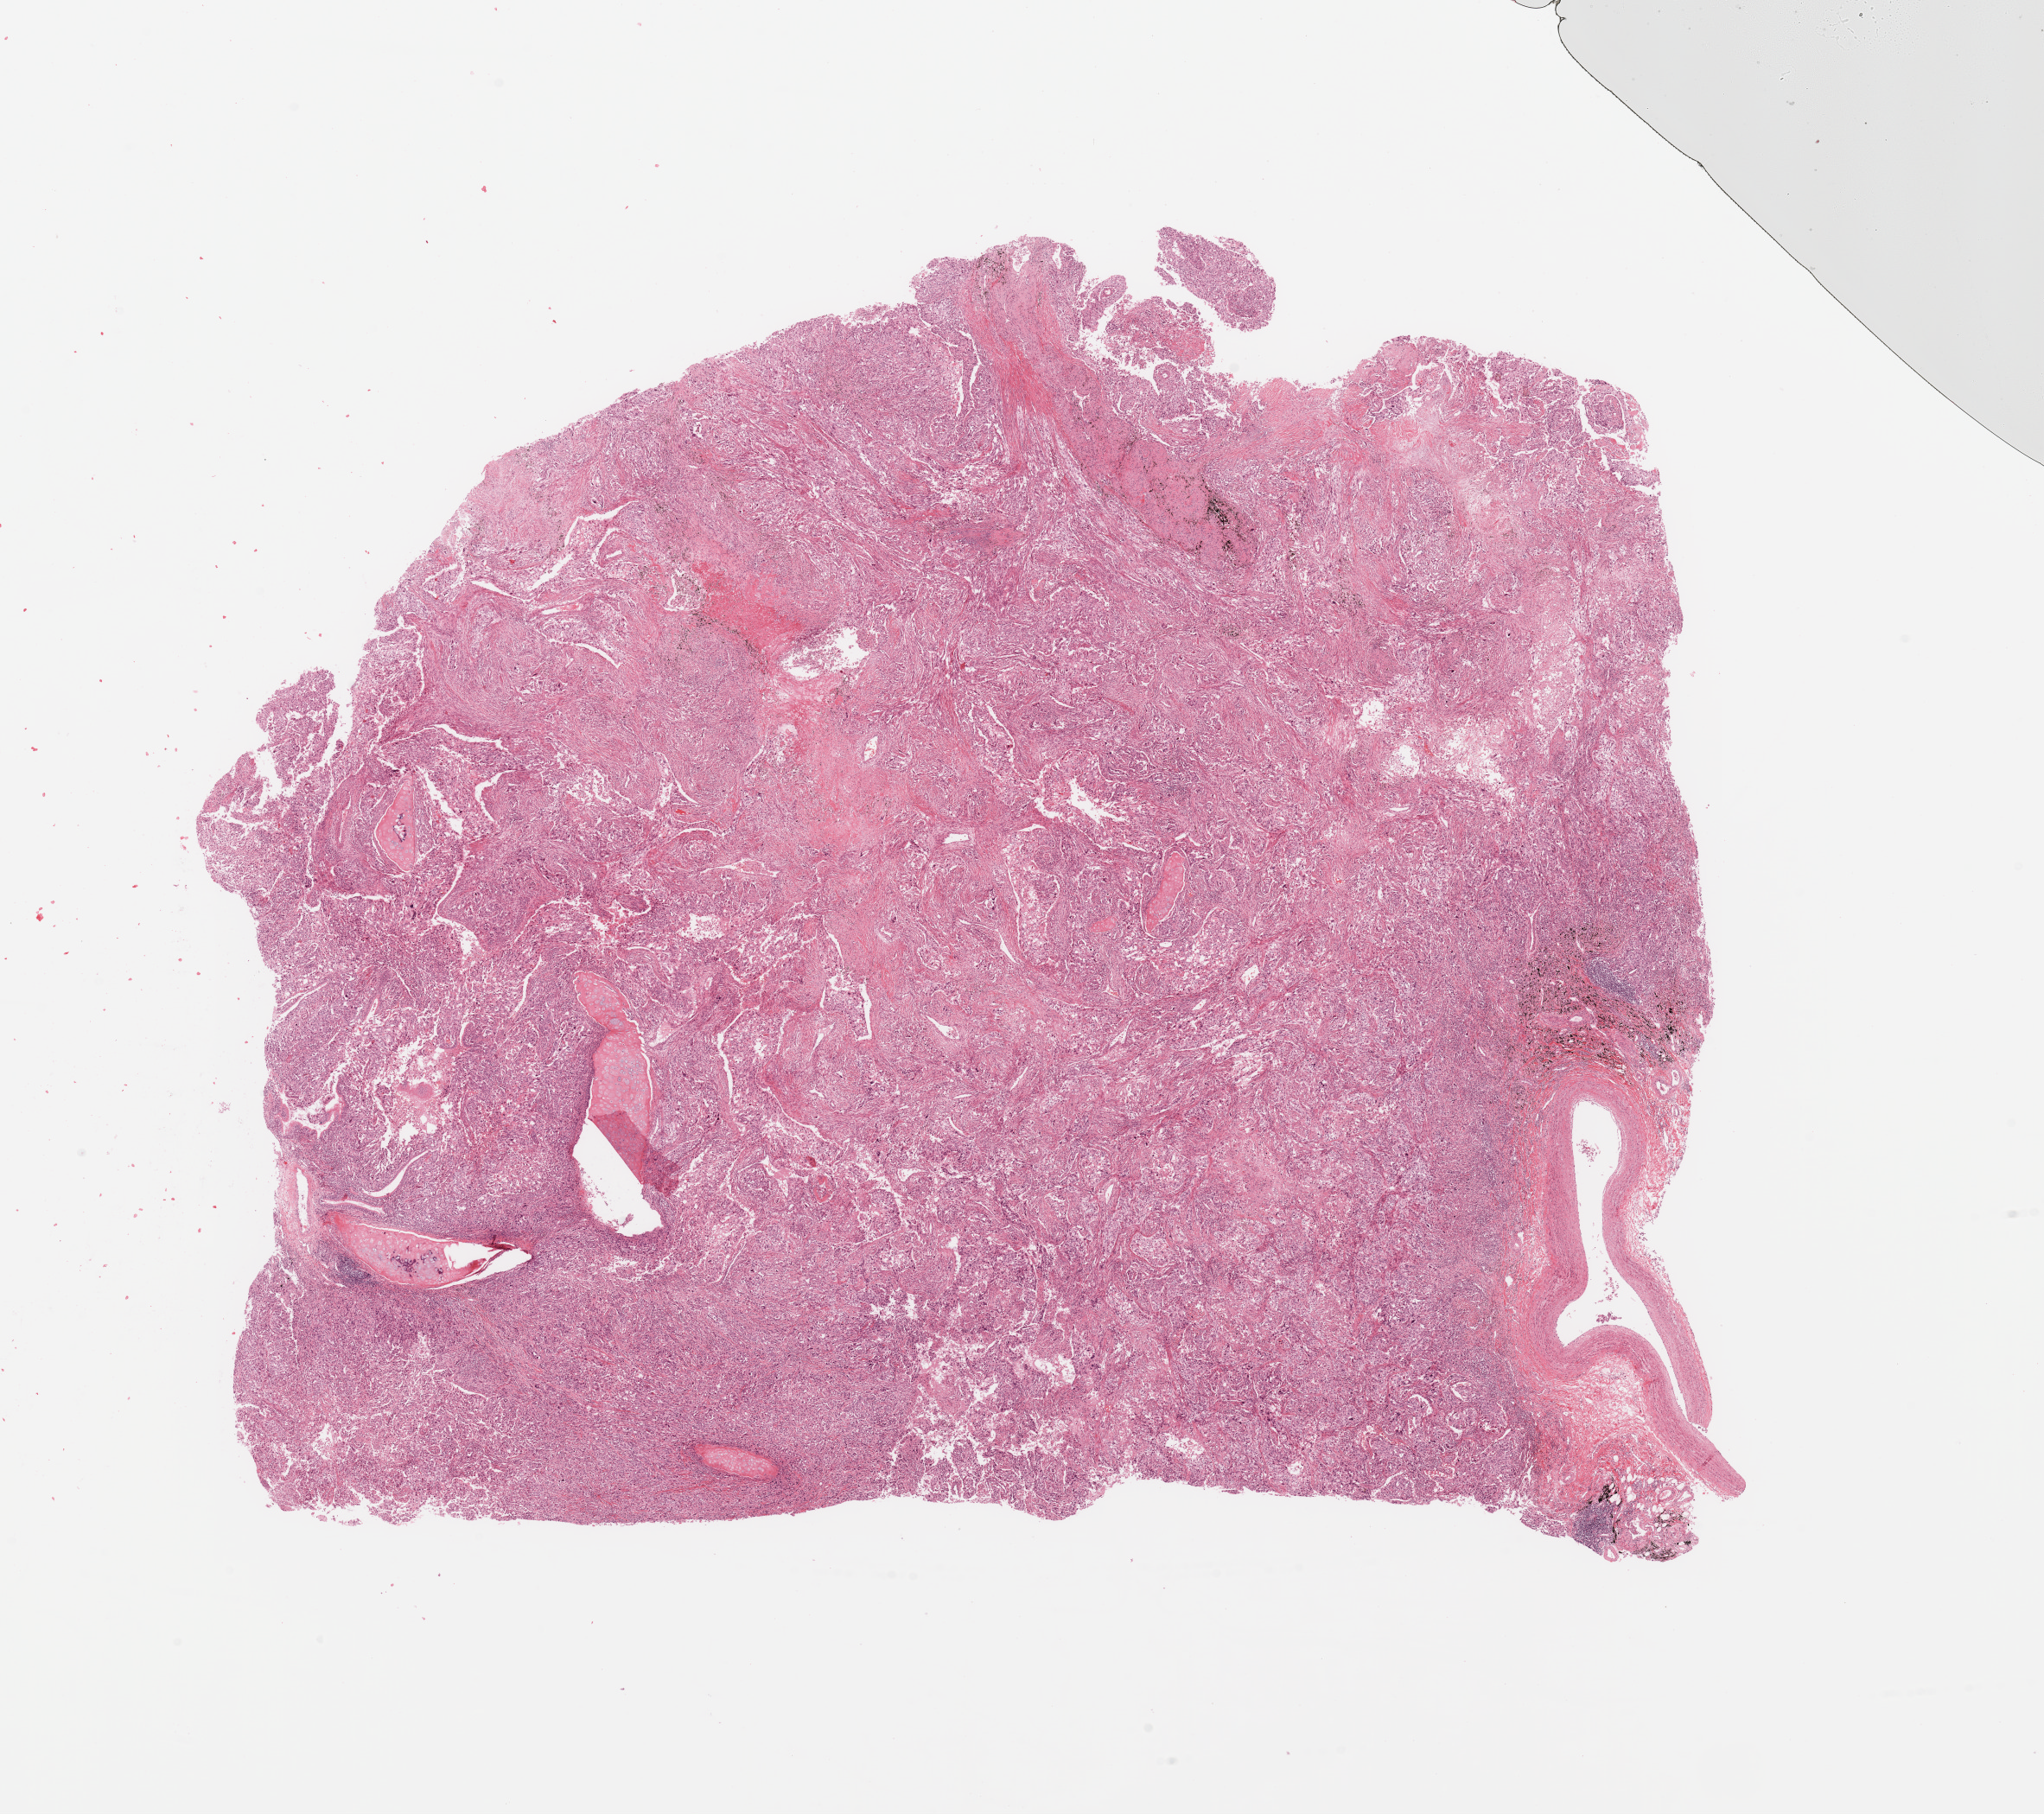
Digitized Hematoxylin and eosin (H&E) stained tissue section (whole slide), whole scanned area (about 18.7 x 16.6 mm) shown as a low-resolution overview, tumour tissue sample, sampled site: lung. Male, 69 y/o. Histologic grade: G3 (poorly differentiated). Slide review estimates, as recorded: tumour nuclei 65%, necrosis 15%.
Histologic diagnosis: Adenocarcinoma, NOS. AJCC pathologic stage: IIB.